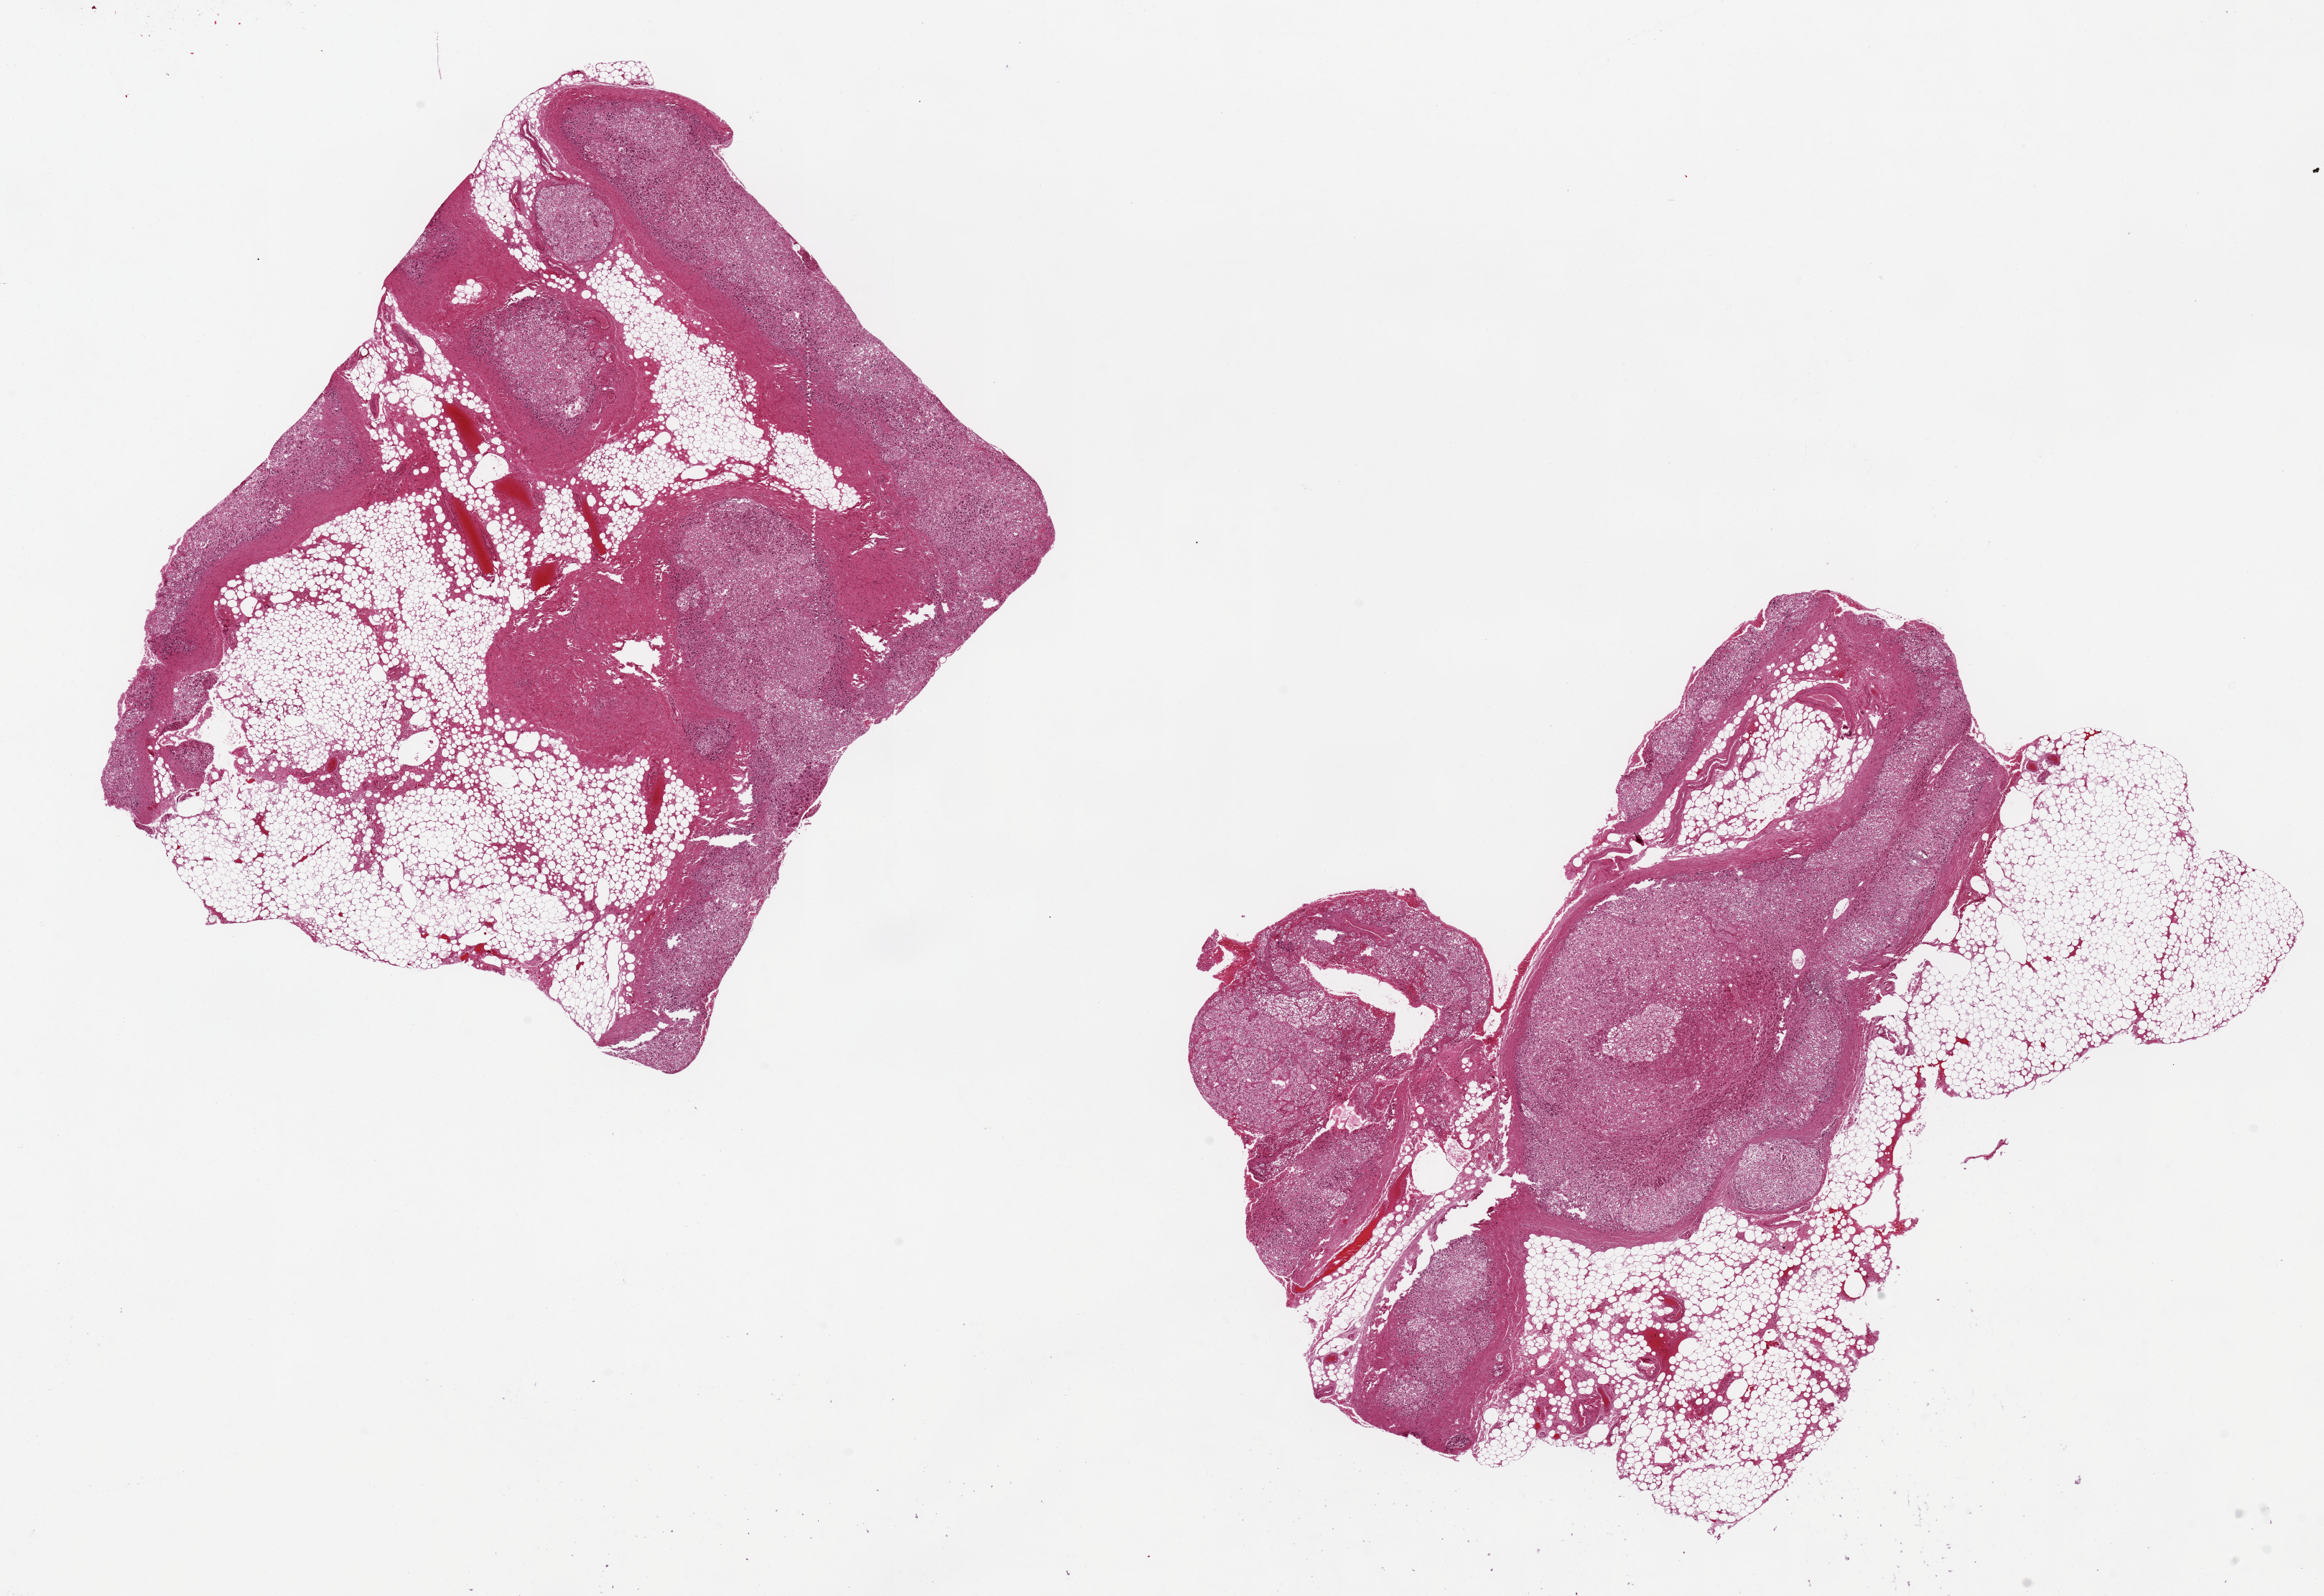
Whole-slide image, H&E stain, a low-resolution overview of the entire scanned area, about 25.6 x 17.6 mm (slide scanned at 20x). Female donor.
Specimen: PAXgene-fixed, paraffin-embedded tissue; sampled site (target tissue): adrenal gland; donor tissue sample.